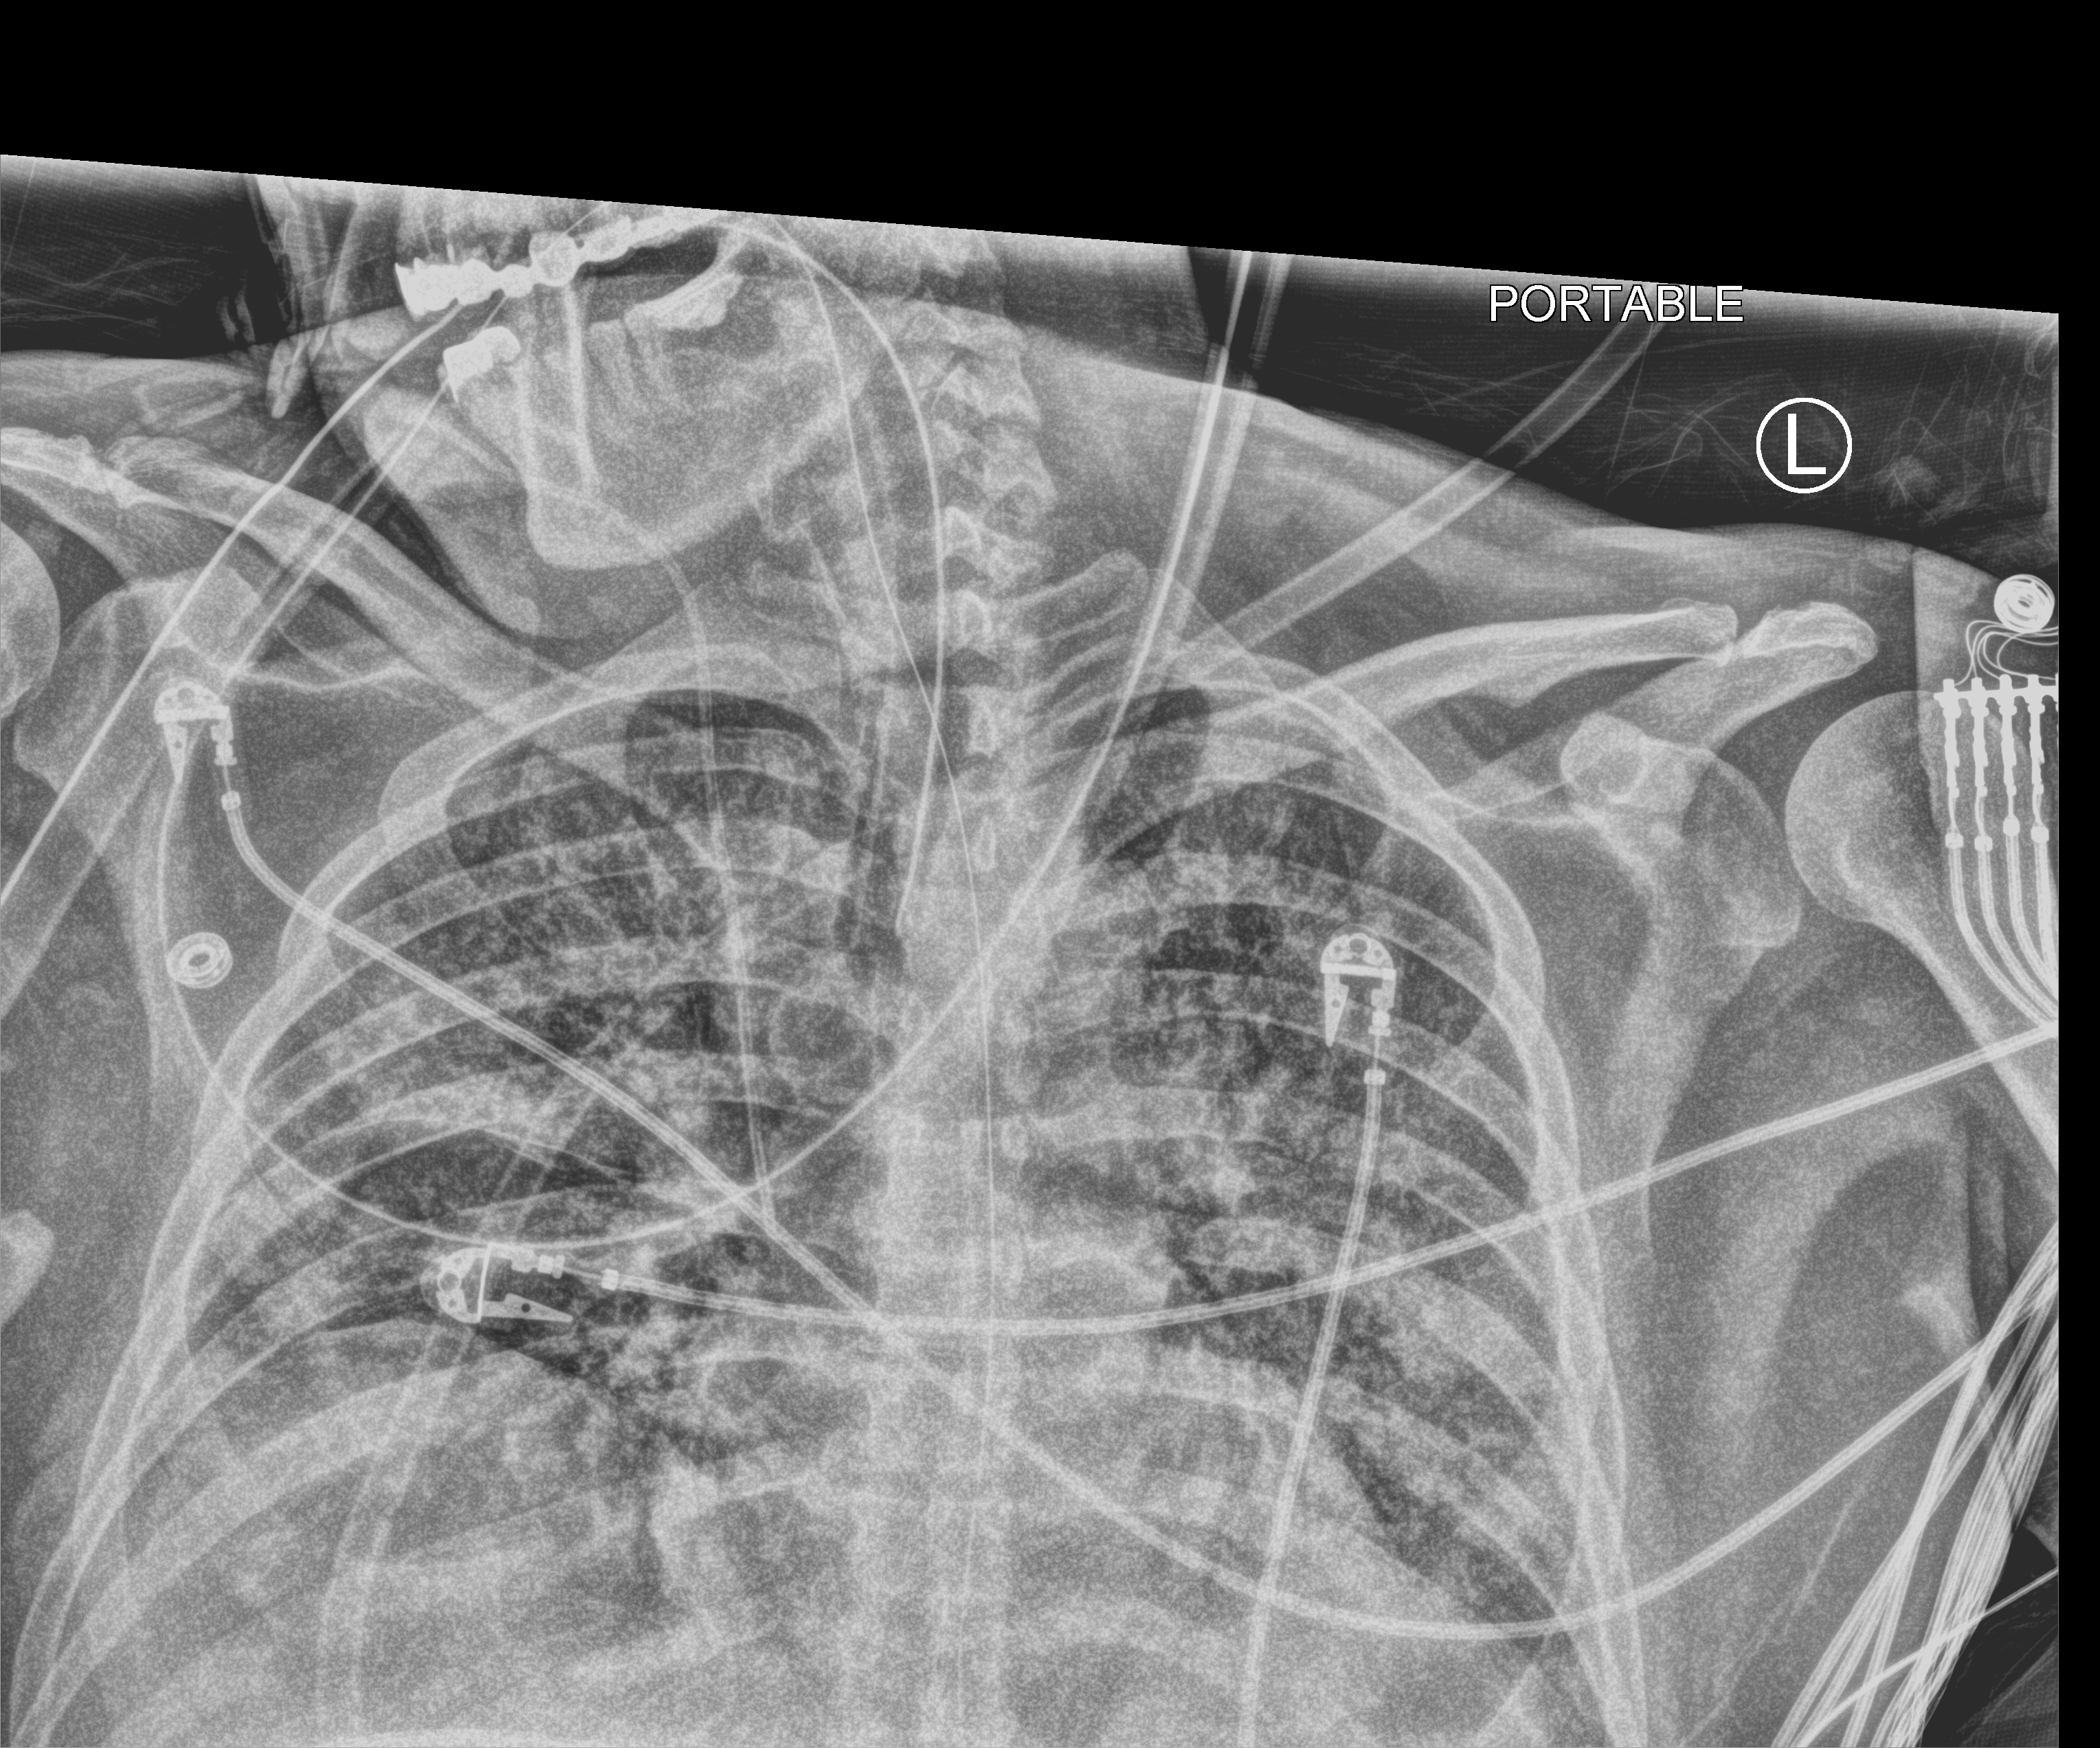
Bedside chest radiograph (computed radiography), anteroposterior (AP) projection. Male patient hospitalised with COVID-19, age 18–59 years.
From the hospital-stay record, not from the radiograph (when in the stay this image was taken is not recorded): mechanically ventilated during this hospital stay: yes; other chronic lung disease (admission record): no.